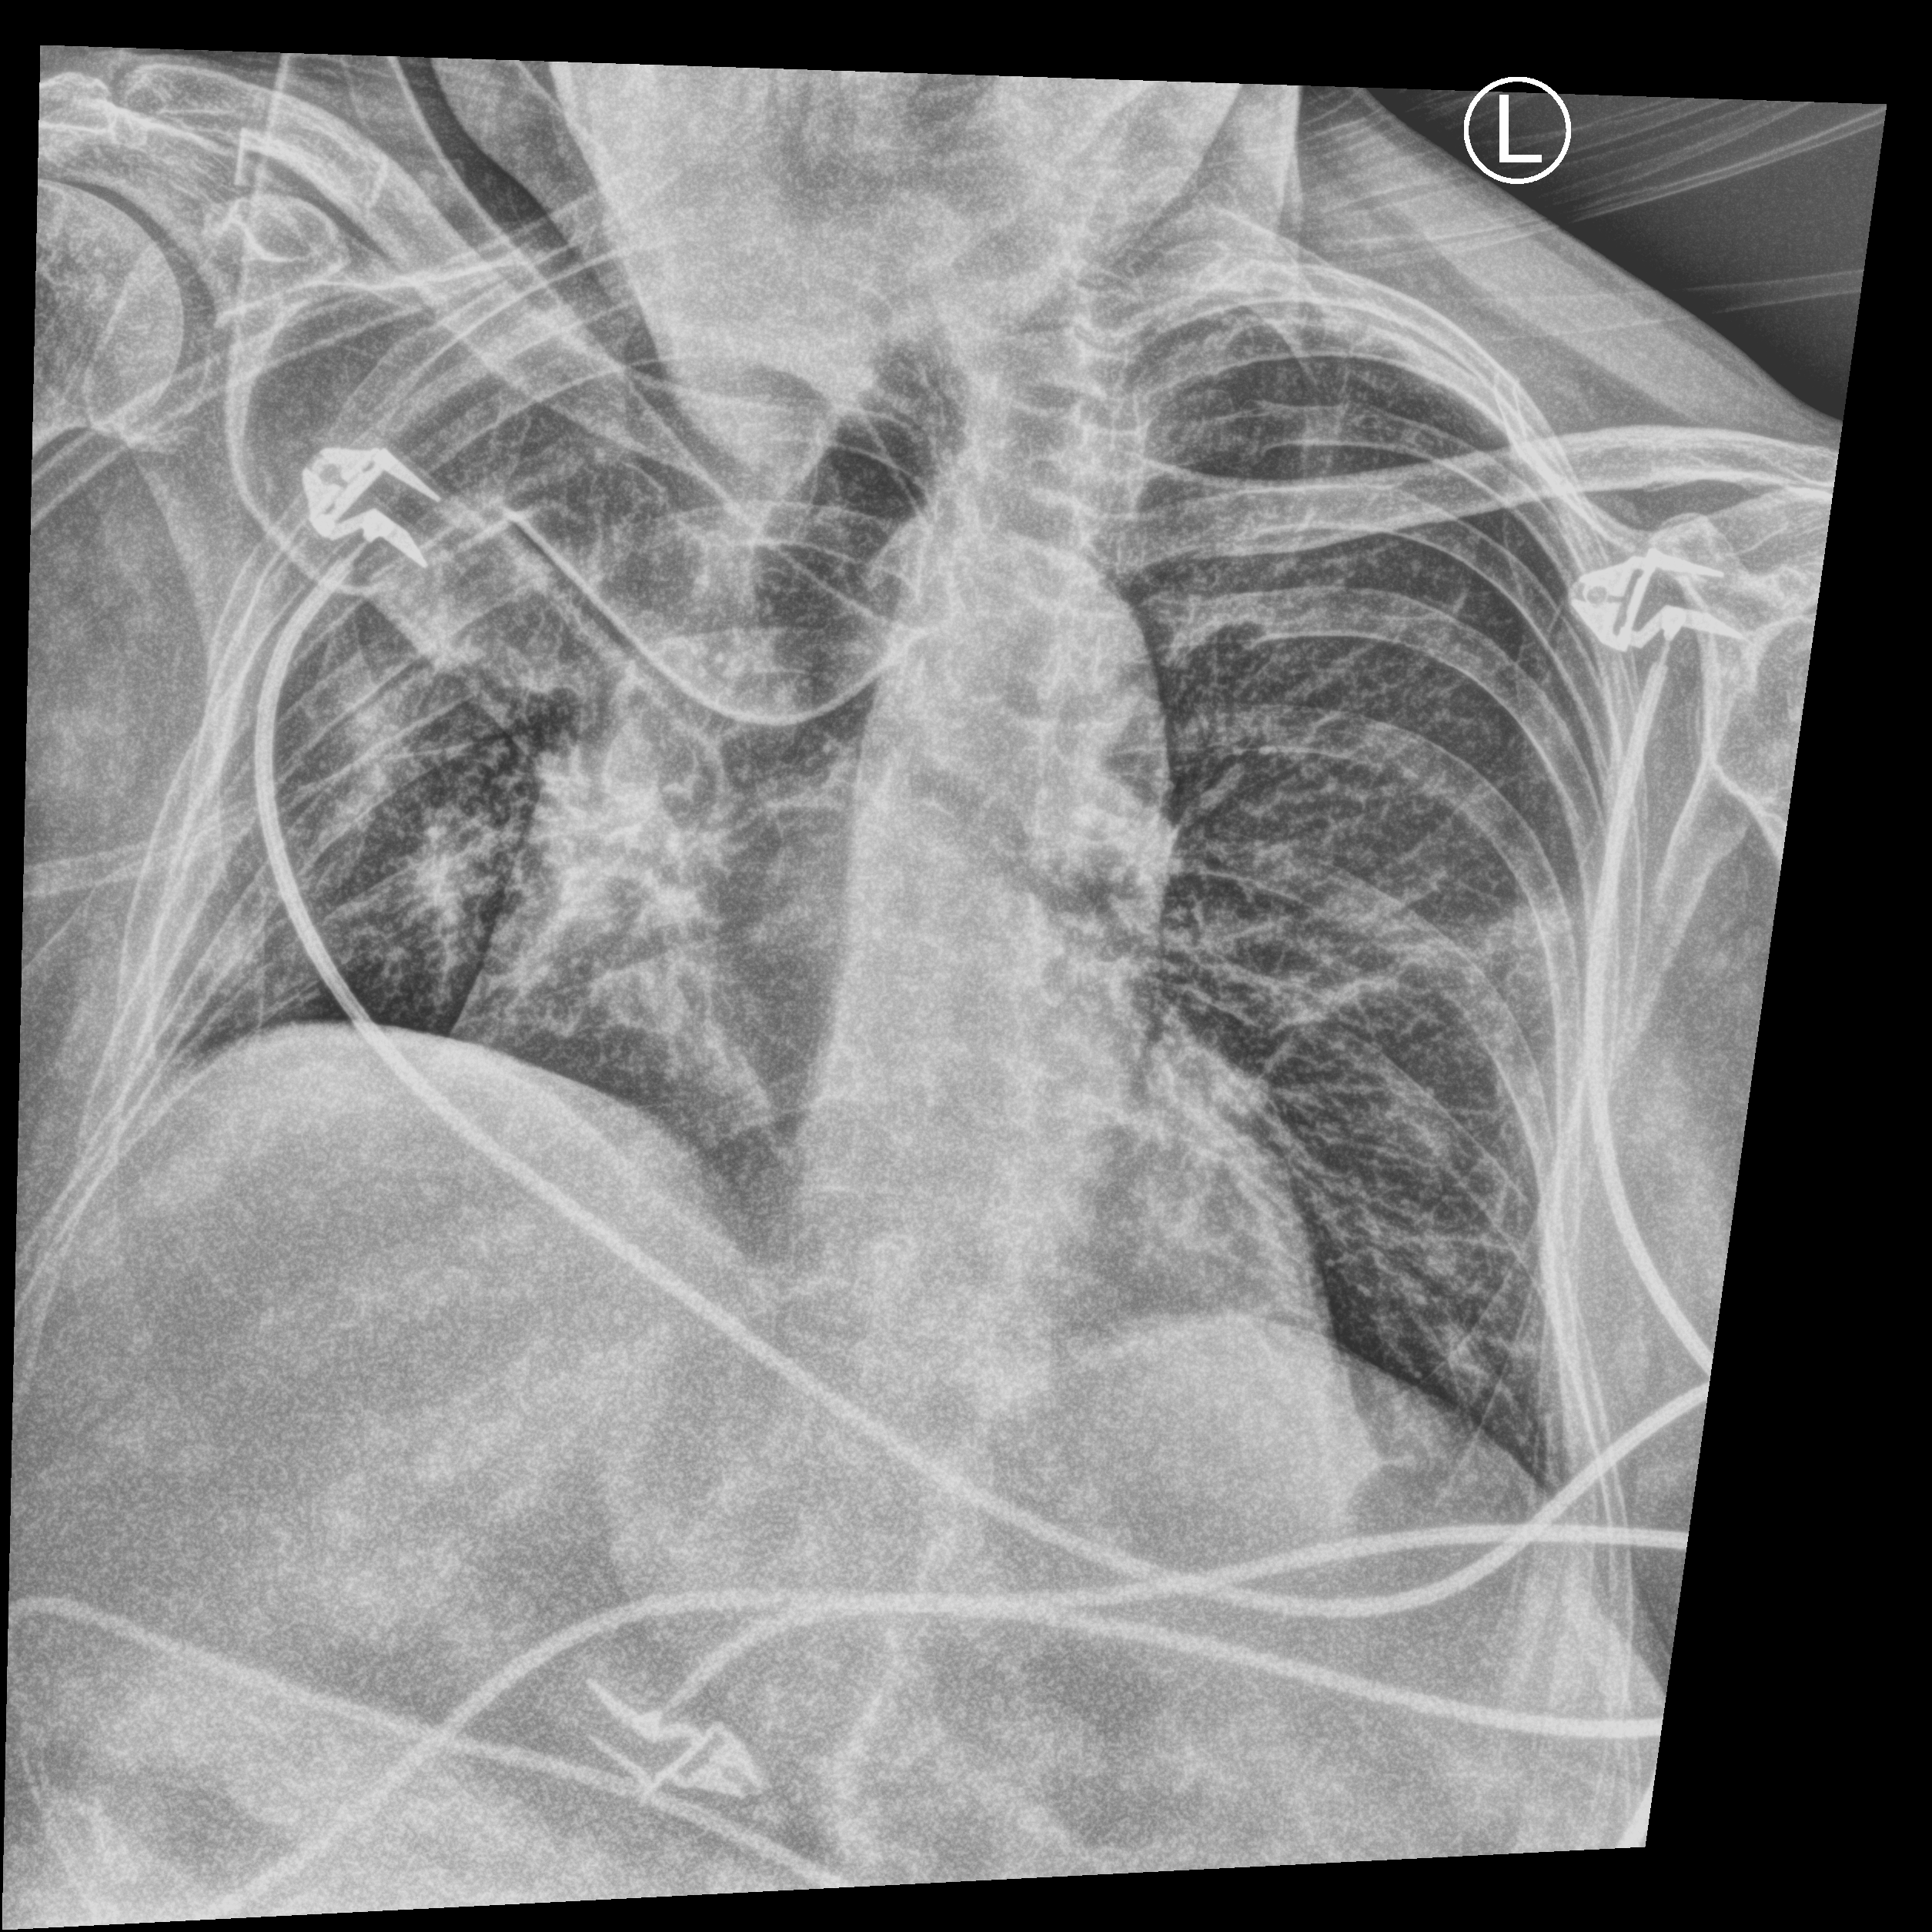
Chest X-ray (portable), anteroposterior (AP) projection. Patient hospitalised with COVID-19; female, aged 75–90 years.
Hospital-stay facts (about this admission, not read from this image; timing relative to this image not recorded):
- mechanically ventilated during this hospital stay: yes
- admitted to intensive care during this hospital stay: yes